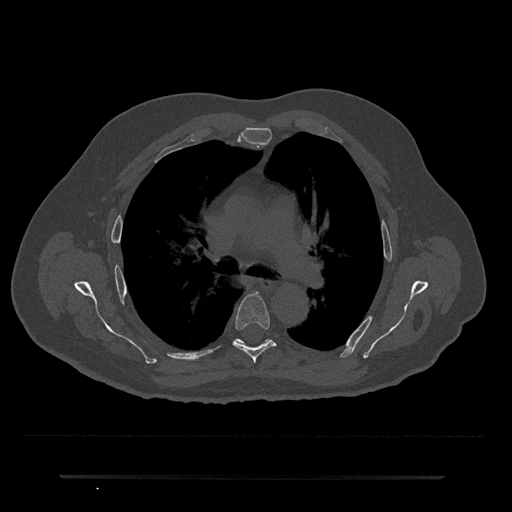
CT including the spine, one axial slice. Slice 476 of 797 in the series (ordered by position). Reconstruction kernel Br40s/3. 120 kVp. Bone window (W 1800 / L 400 HU). 0.5 mm slice thickness. 512 × 512 image matrix, field of view 437 × 437 mm. Patient: male, 69 years. Case-level facts recorded for this patient, not image findings: primary cancer: prostate.
Annotated regions visible in this slice (semi-automatically segmented with operator editing):
- T5 vertebra: bounding box <233,293,276,363> (left, top, right, bottom; pixels)